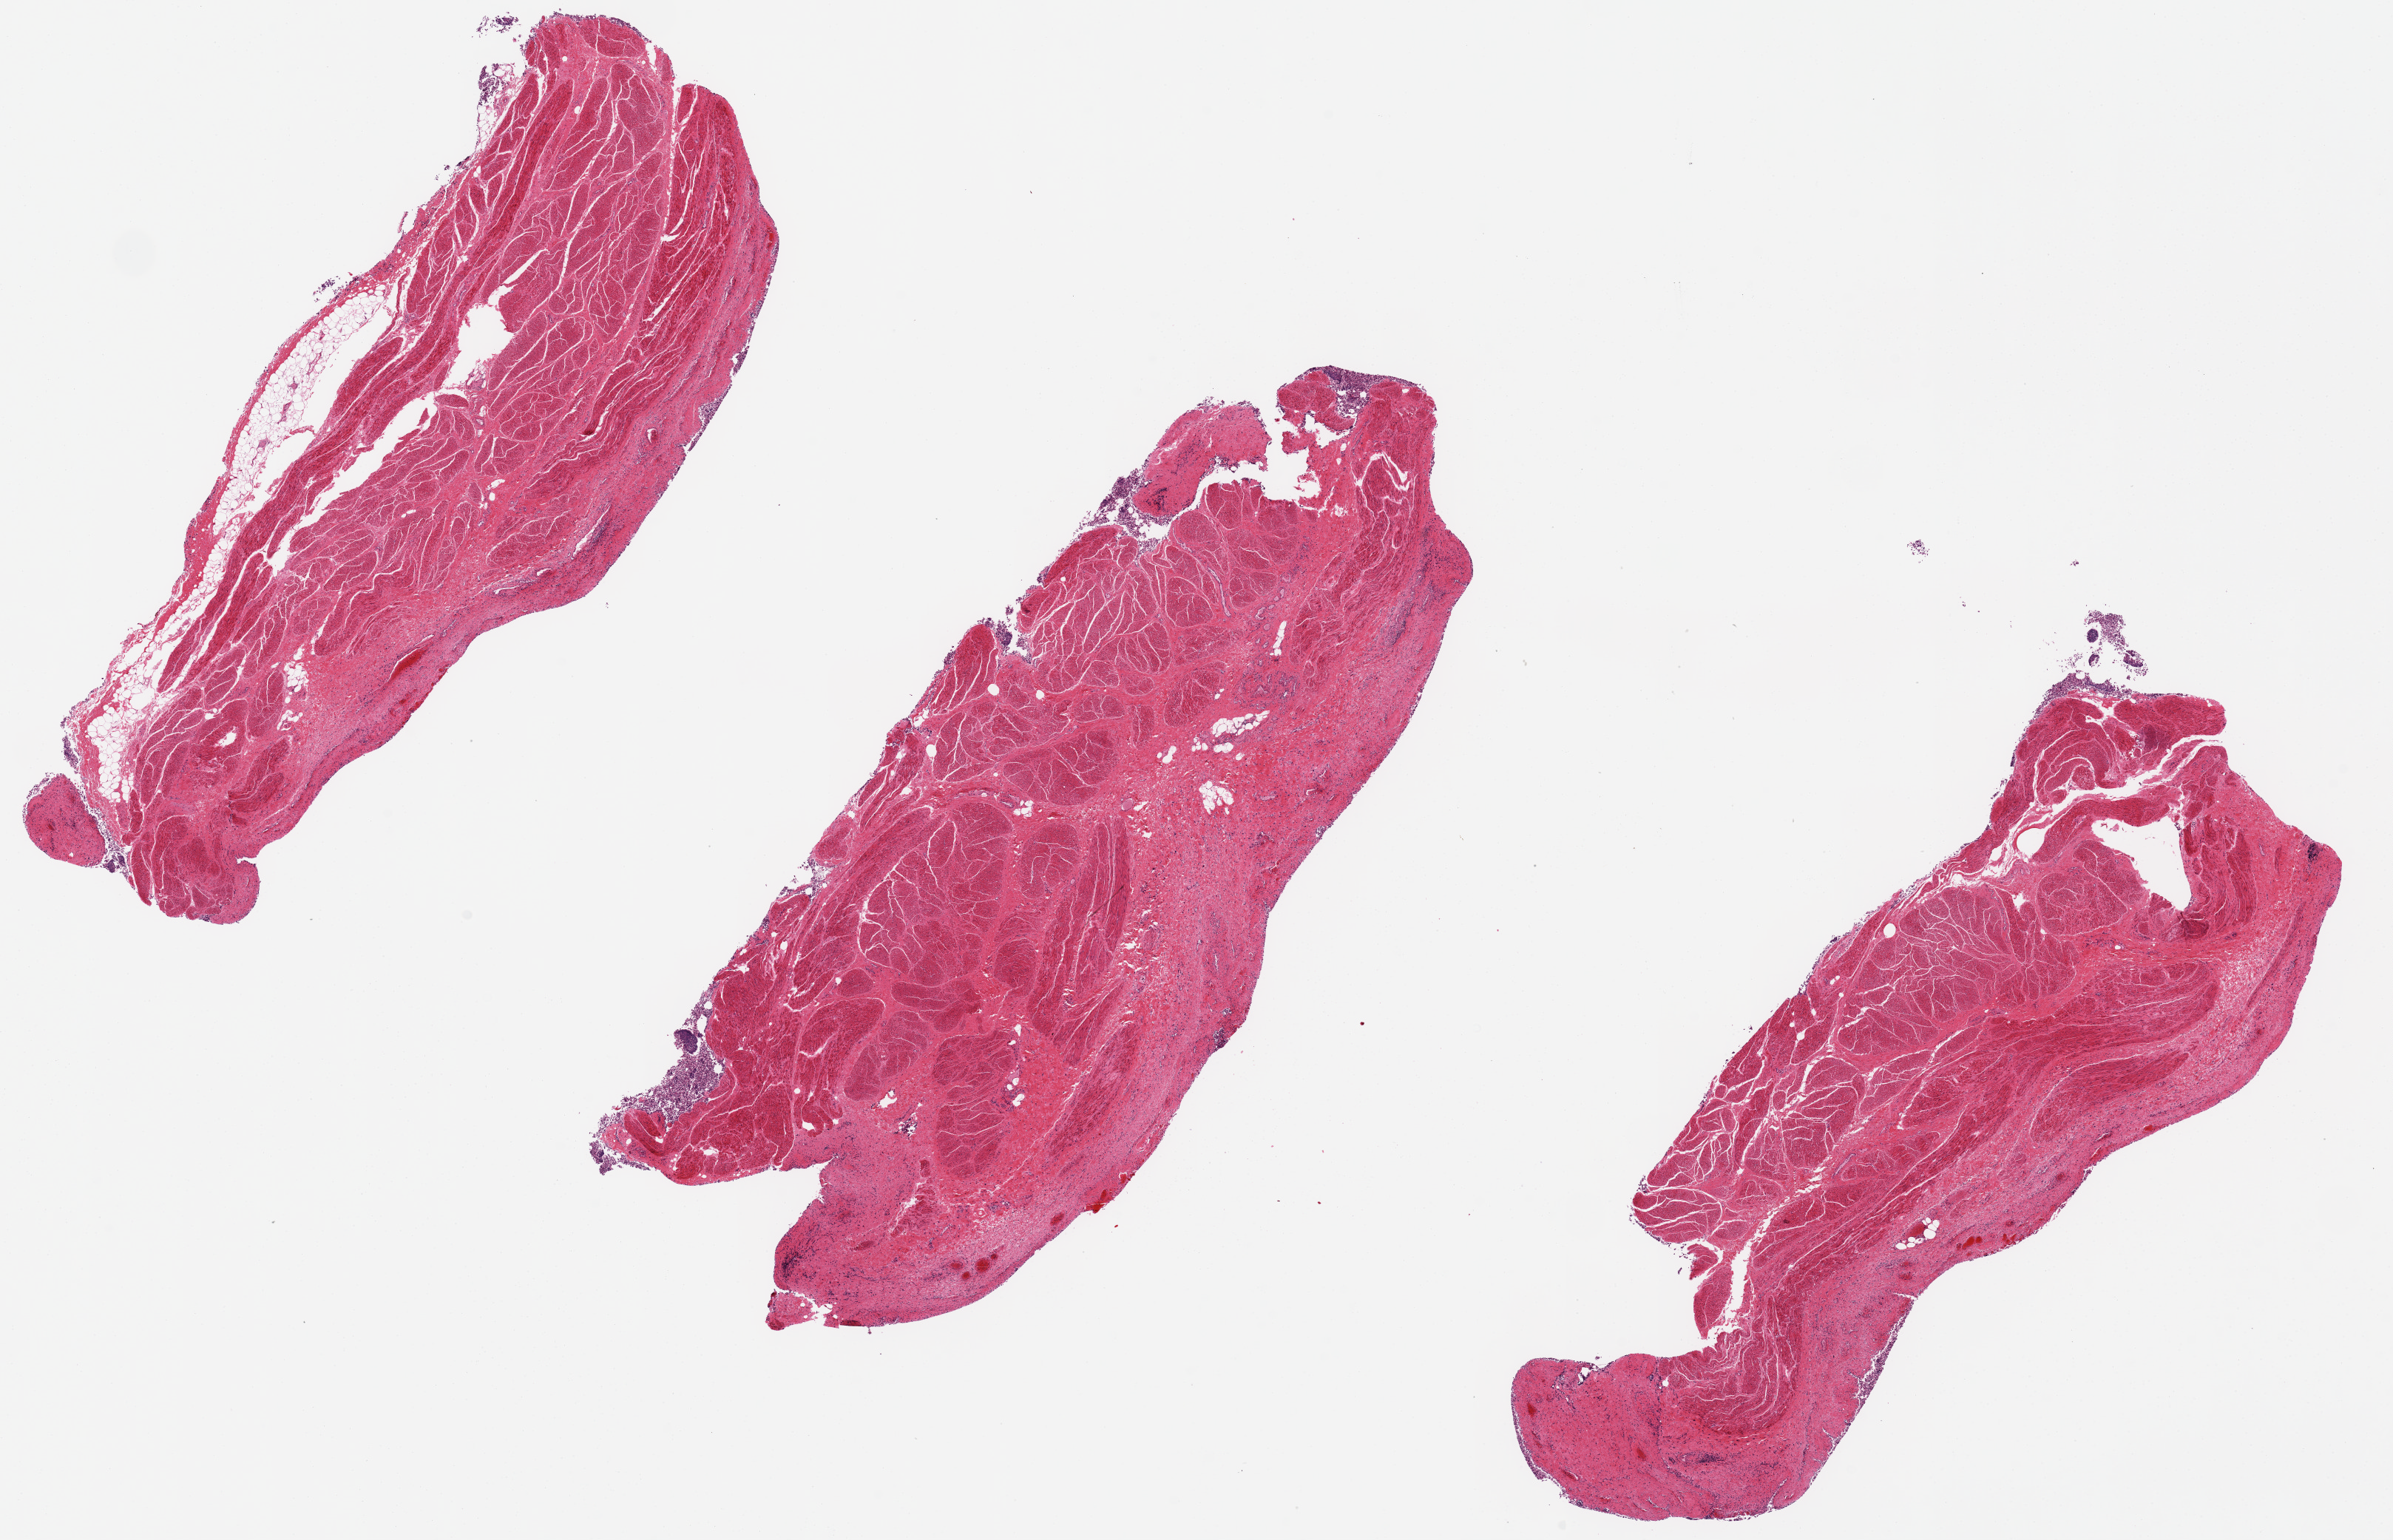
Whole-slide image, haematoxylin and eosin stain, whole scanned area (about 25.6 x 16.5 mm, from a 20x scan) shown as a low-resolution overview. PAXgene-fixed, paraffin-embedded tissue. Section of urinary bladder (target tissue). Donor tissue sample. Donor sex: male.
Pathologist's review note for this sample: epithelium totally autolyzed and sloughed.